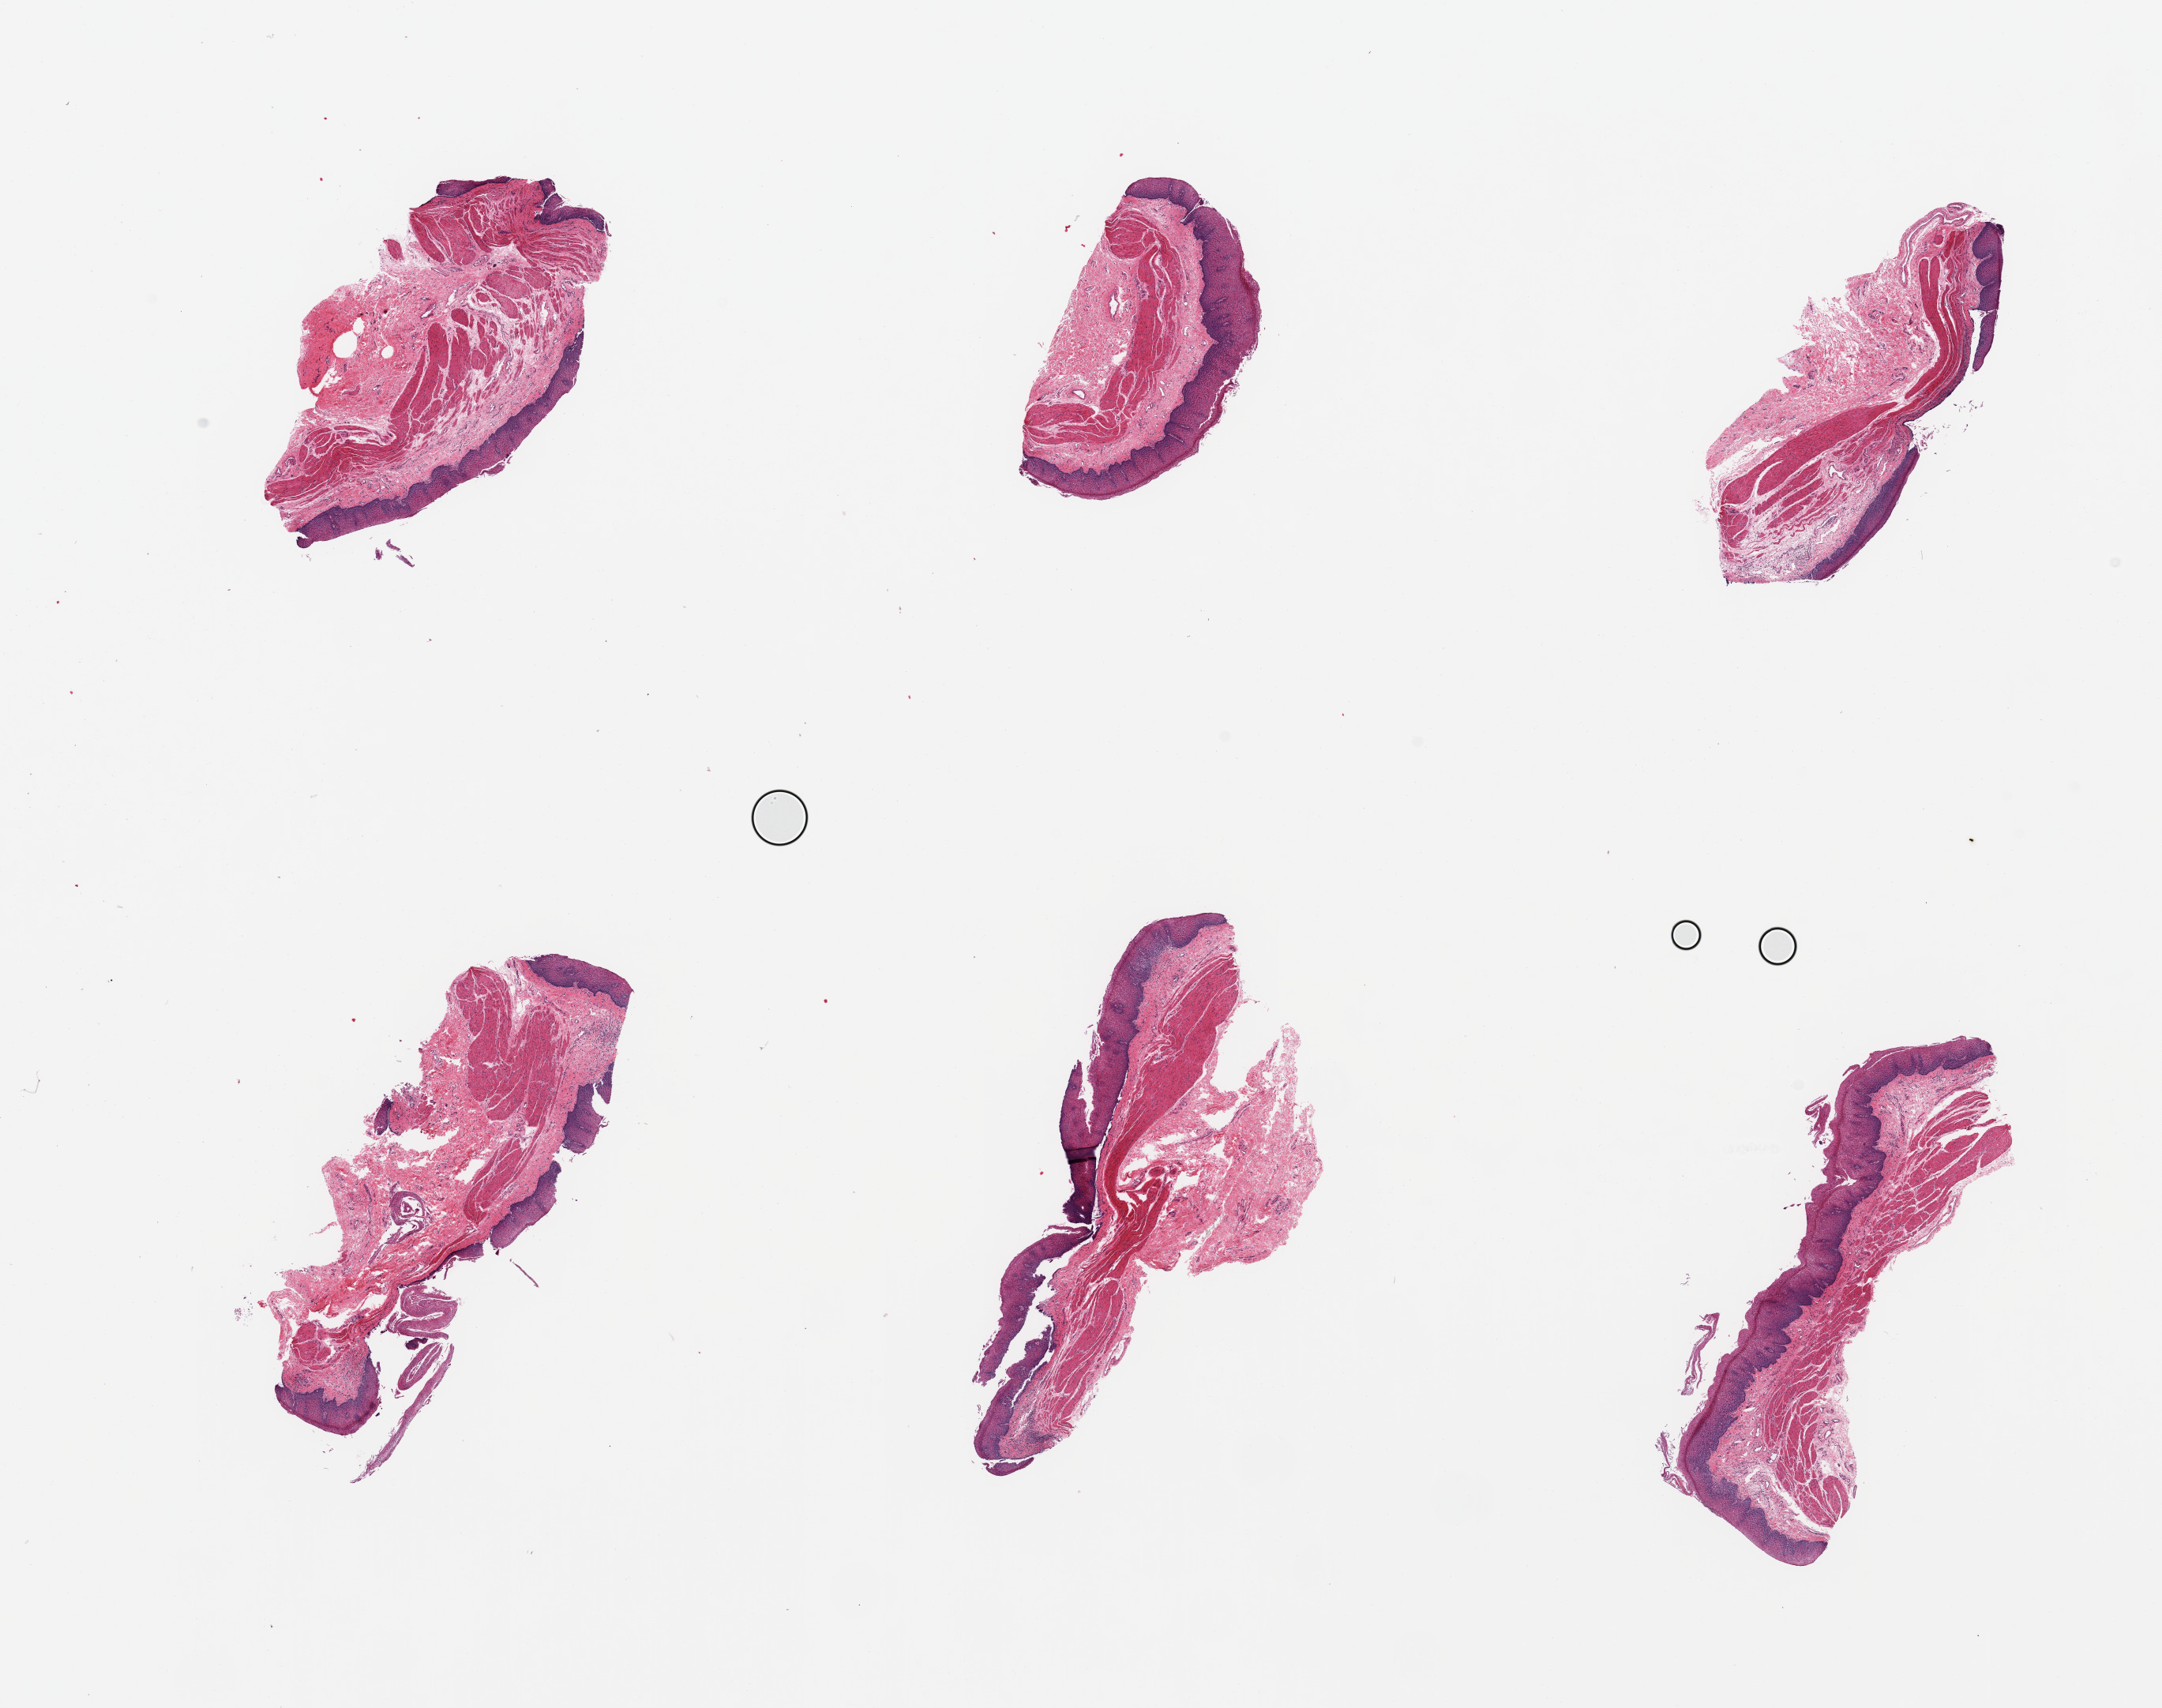
Digitized haematoxylin and eosin-stained section, low-resolution overview of the scanned area, about 21.7 x 17.1 mm (slide scanned at 20x); PAXgene-fixed paraffin-embedded (PFPE) section; target tissue: esophageal mucous membrane; tissue donor sample. Donor: female.
• pathologist's review note for this sample: 6 pieces, squamous mucosa up to ~0.5mm, ~20-30% thickness